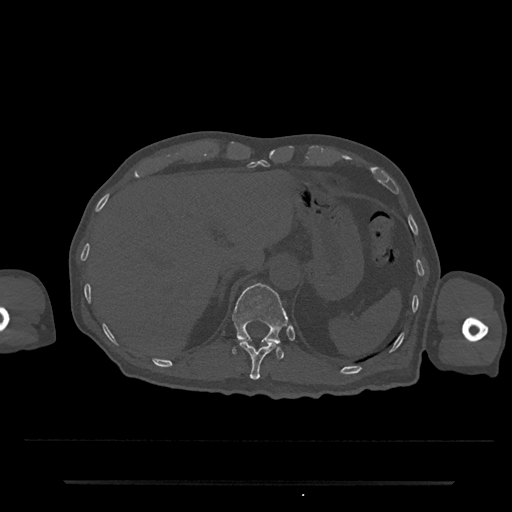
CT including the spine, one axial slice; position 224 of 797 along the scan axis; 120 kVp; bone window (W 1800 / L 400 HU); 0.5 mm slice thickness; 512 × 512 image matrix. Male patient, age 74 years. Case-level facts recorded for this patient, not image findings: primary cancer: prostate.
Annotated regions visible in this slice (semi-automatically segmented with operator editing):
- T11 vertebra: bounding box <238,340,277,380> (left, top, right, bottom; pixels)
- T12 vertebra: <232,283,288,359>